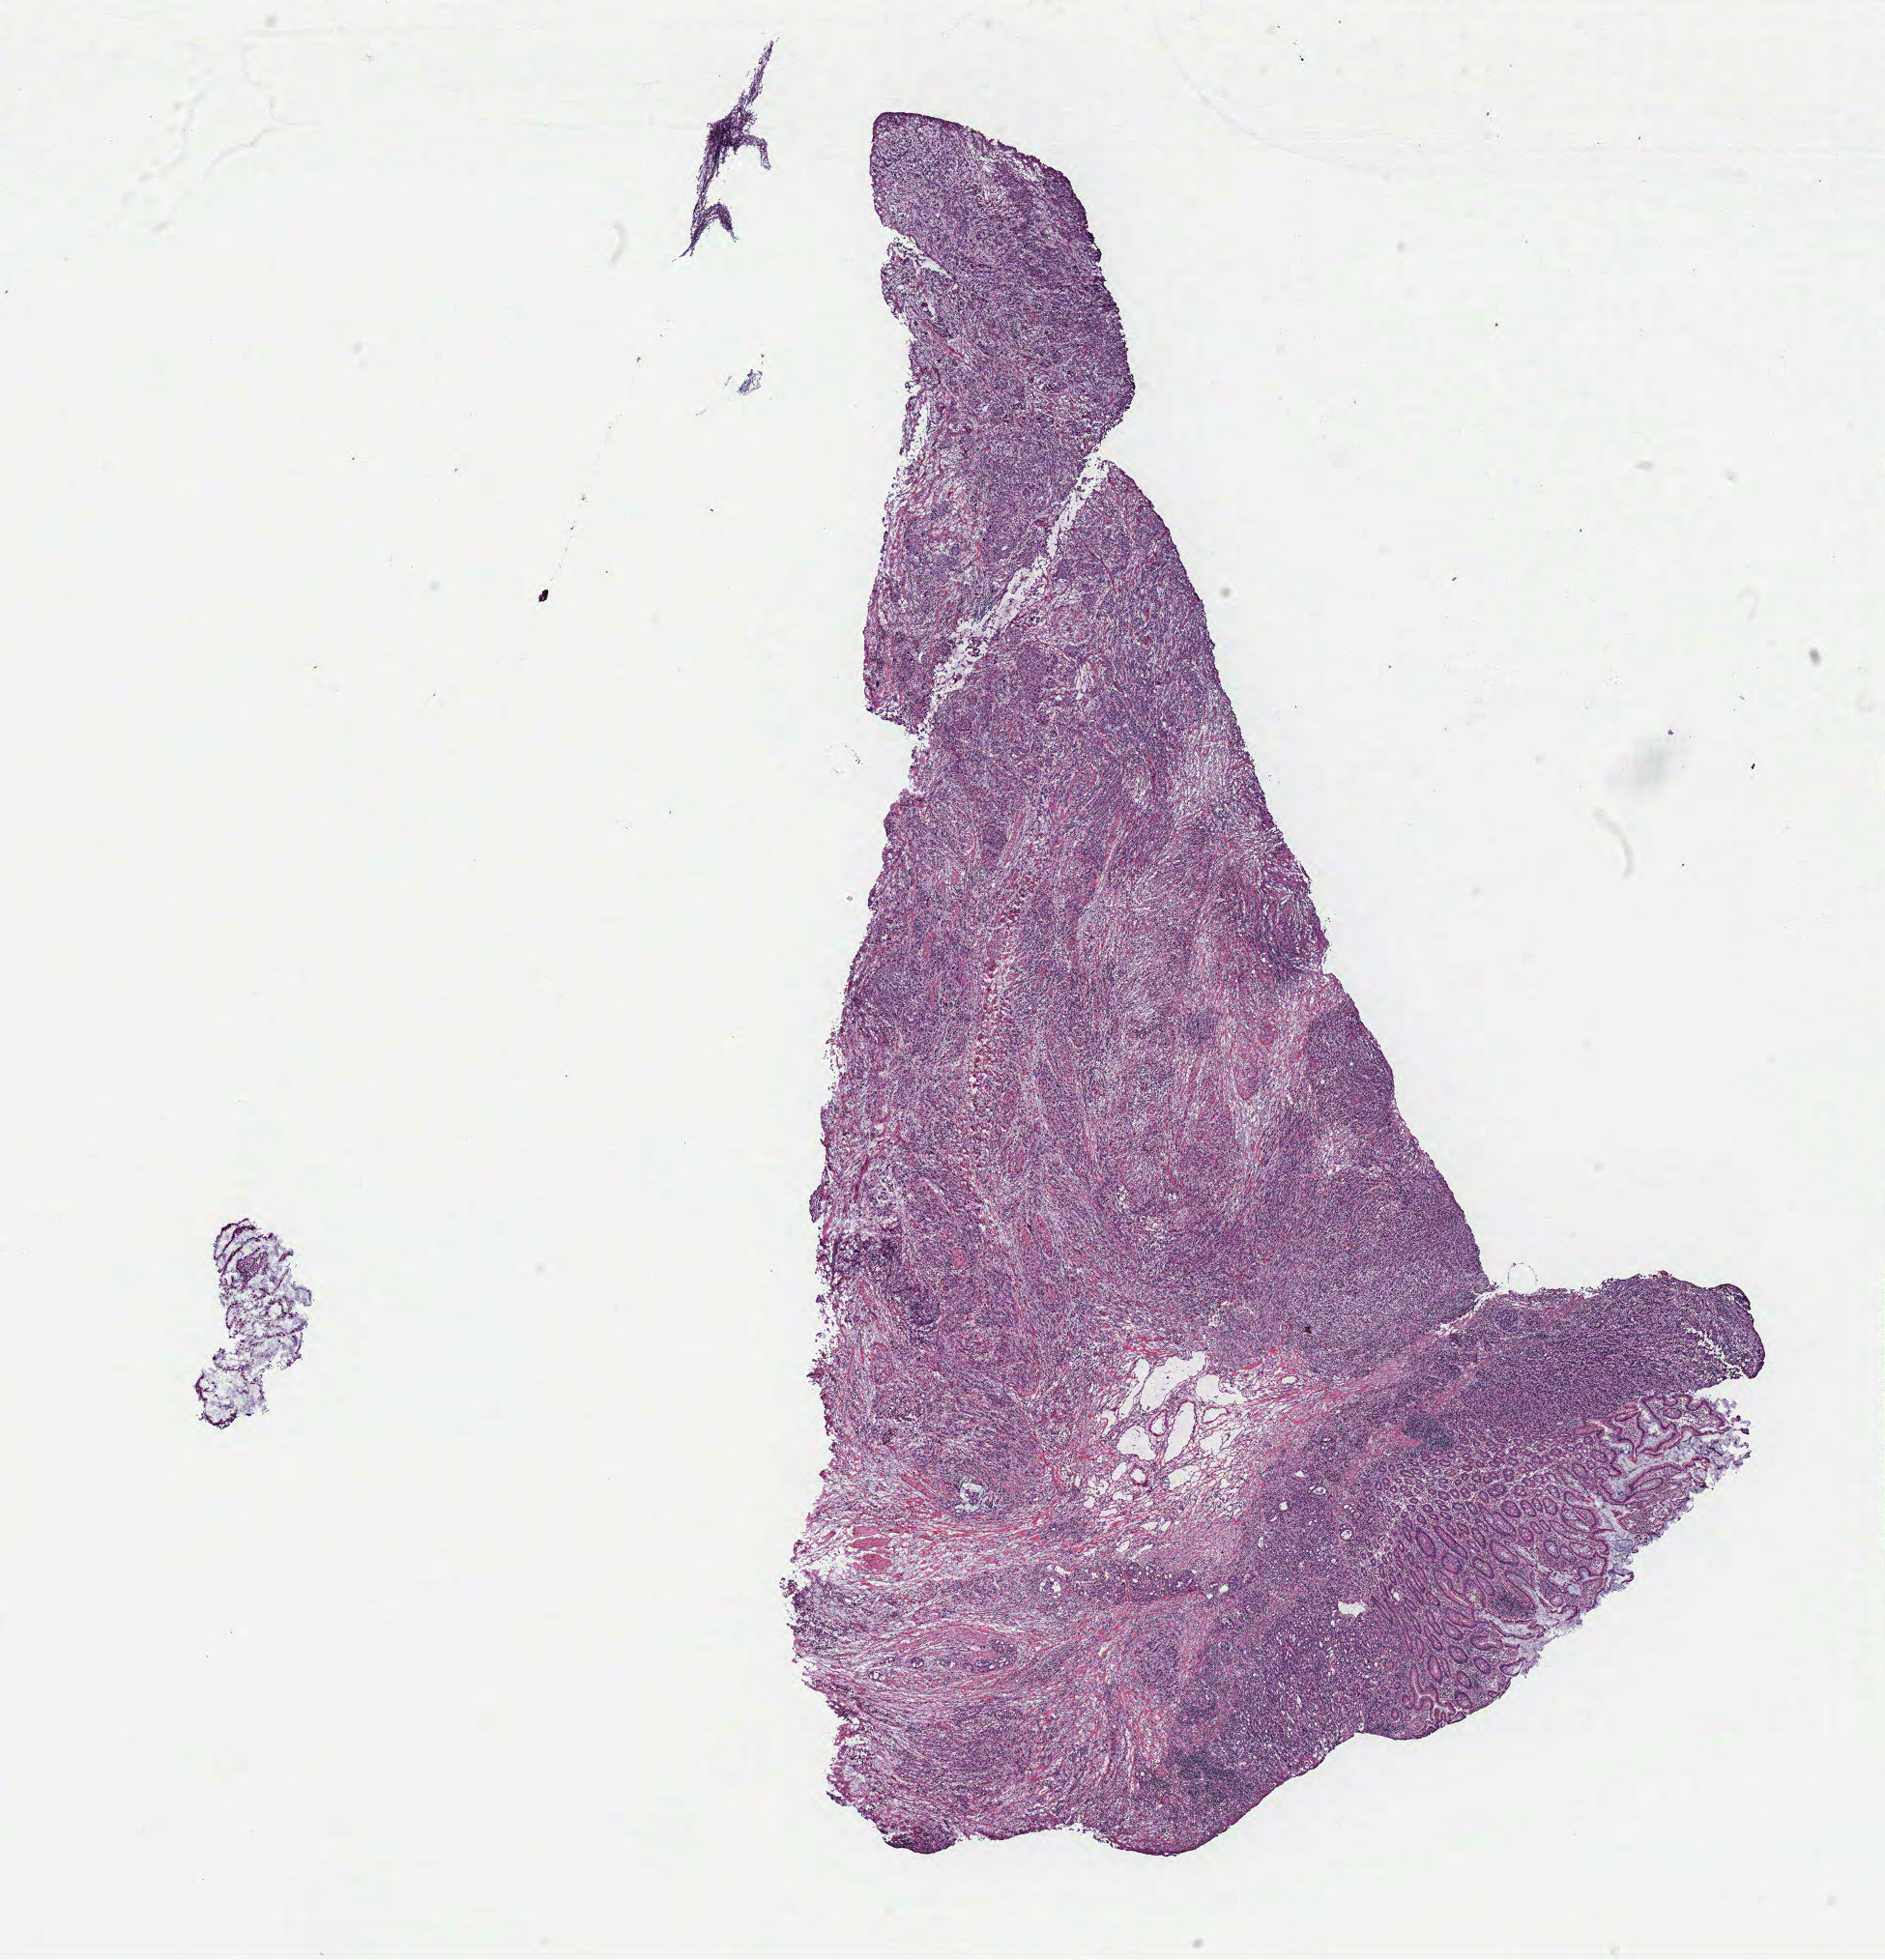
H&E-stained whole-slide image, whole scanned area (about 15.6 x 16.2 mm, from a 40x scan) shown as a low-resolution overview; normal (non-tumour) tissue sample, colon. Female, 57 y/o.
• this section: normal (non-tumour) tissue from the same patient
• patient diagnosis: Adenocarcinoma, NOS